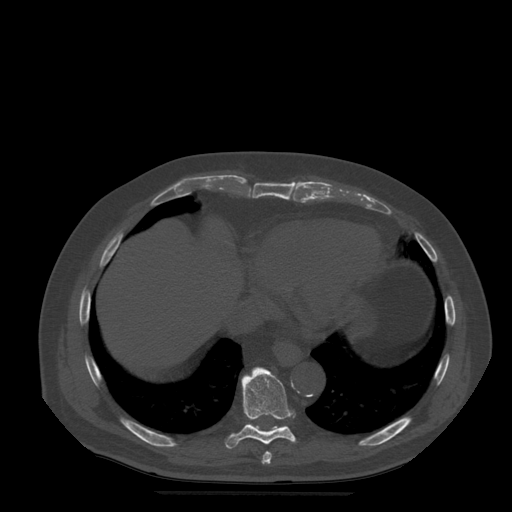
CT including the spine, one axial slice; slice 289 of 522 in the series (ordered by position); bone window (W 1800 / L 400 HU); 512 × 512 image matrix. Patient age 72 years. Case-level facts recorded for this patient, not image findings: primary cancer: prostate.
Outlined on this slice (semi-automatic segmentation, software-assisted and operator-edited):
- T8 vertebra: bounding box [x1, y1, x2, y2] px = [262, 452, 272, 464]
- T9 vertebra: [225, 367, 297, 449]